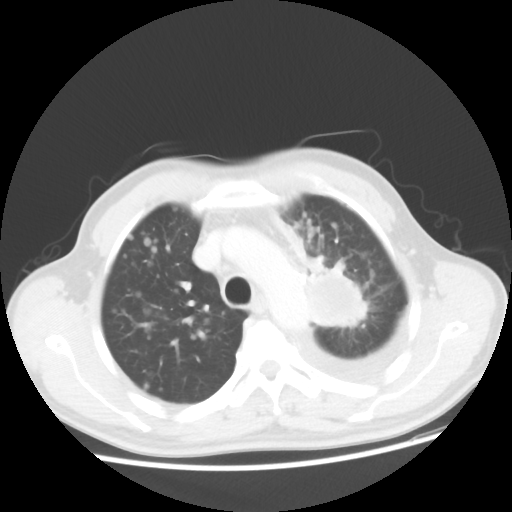
Chest CT, one axial slice. 100 kVp. Lung window (W 1500 / L -600 HU). 5 mm slice thickness. 512 × 512 image matrix, field of view 362 × 362 mm. Male patient, age 55 years. Case-level facts recorded for this patient, not image findings: clinical TNM (as recorded): T2 N3 M1a; histopathological grade: G3.
Structures marked on this image (bounding box drawn by a radiologist):
- lung tumour (recorded histology: squamous cell carcinoma): bounding box (x1, y1, x2, y2) in pixels: (306, 252, 375, 343)